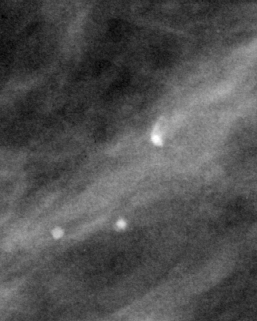
Cropped region of a digitized screen-film mammogram centred on a radiologist-marked abnormality; right breast; MLO view.
Calcifications, morphology pleomorphic, distribution clustered; BI-RADS assessment category 2; benign; no additional work-up was recommended (benign without callback).